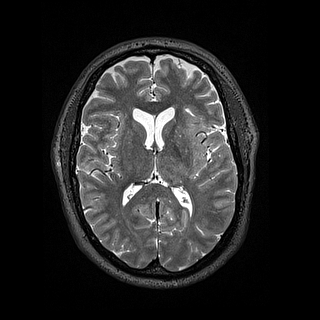
Brain MRI from a brain-tumour surgery series, one axial slice. Slice 78 of 144 in the series (ordered by position). 1.2 mm slice thickness. 320 × 320 image matrix. Case-level facts recorded for this patient, not image findings: histopathology: Astrocytoma; WHO grade: 2; IDH mutation: yes.
Annotated regions visible in this slice (expert manual segmentation):
- tumour: bounding box (x1, y1, x2, y2) in pixels: (190, 143, 208, 177)